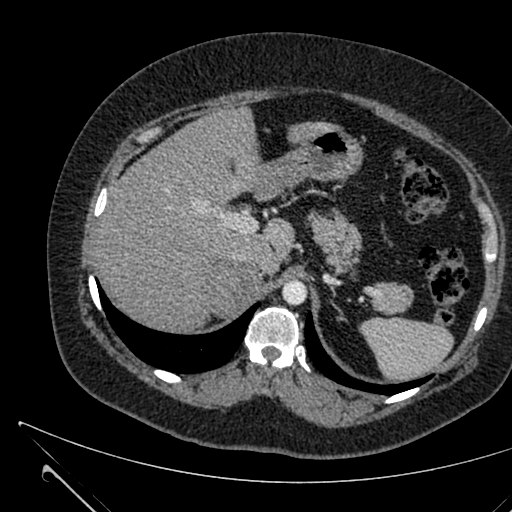
Contrast-enhanced abdominal CT, one axial slice. Slice 476 of 731 in the series (ordered by position). Soft-tissue window (W 400 / L 40 HU). 1 mm slice thickness. 512 × 512 image matrix. Patient: female, 36 years. Case-level facts recorded for this patient, not image findings: diagnosis: adrenocortical carcinoma; tumour side: right adrenal; tumour size at pathology: 10 cm; Ki-67 index: 20 %; stage (as recorded): 4.
Structures marked on this image (semi-automatic segmentation, software-assisted and operator-edited):
- mass: bounding box (x1, y1, x2, y2) in pixels: (208, 263, 262, 316)